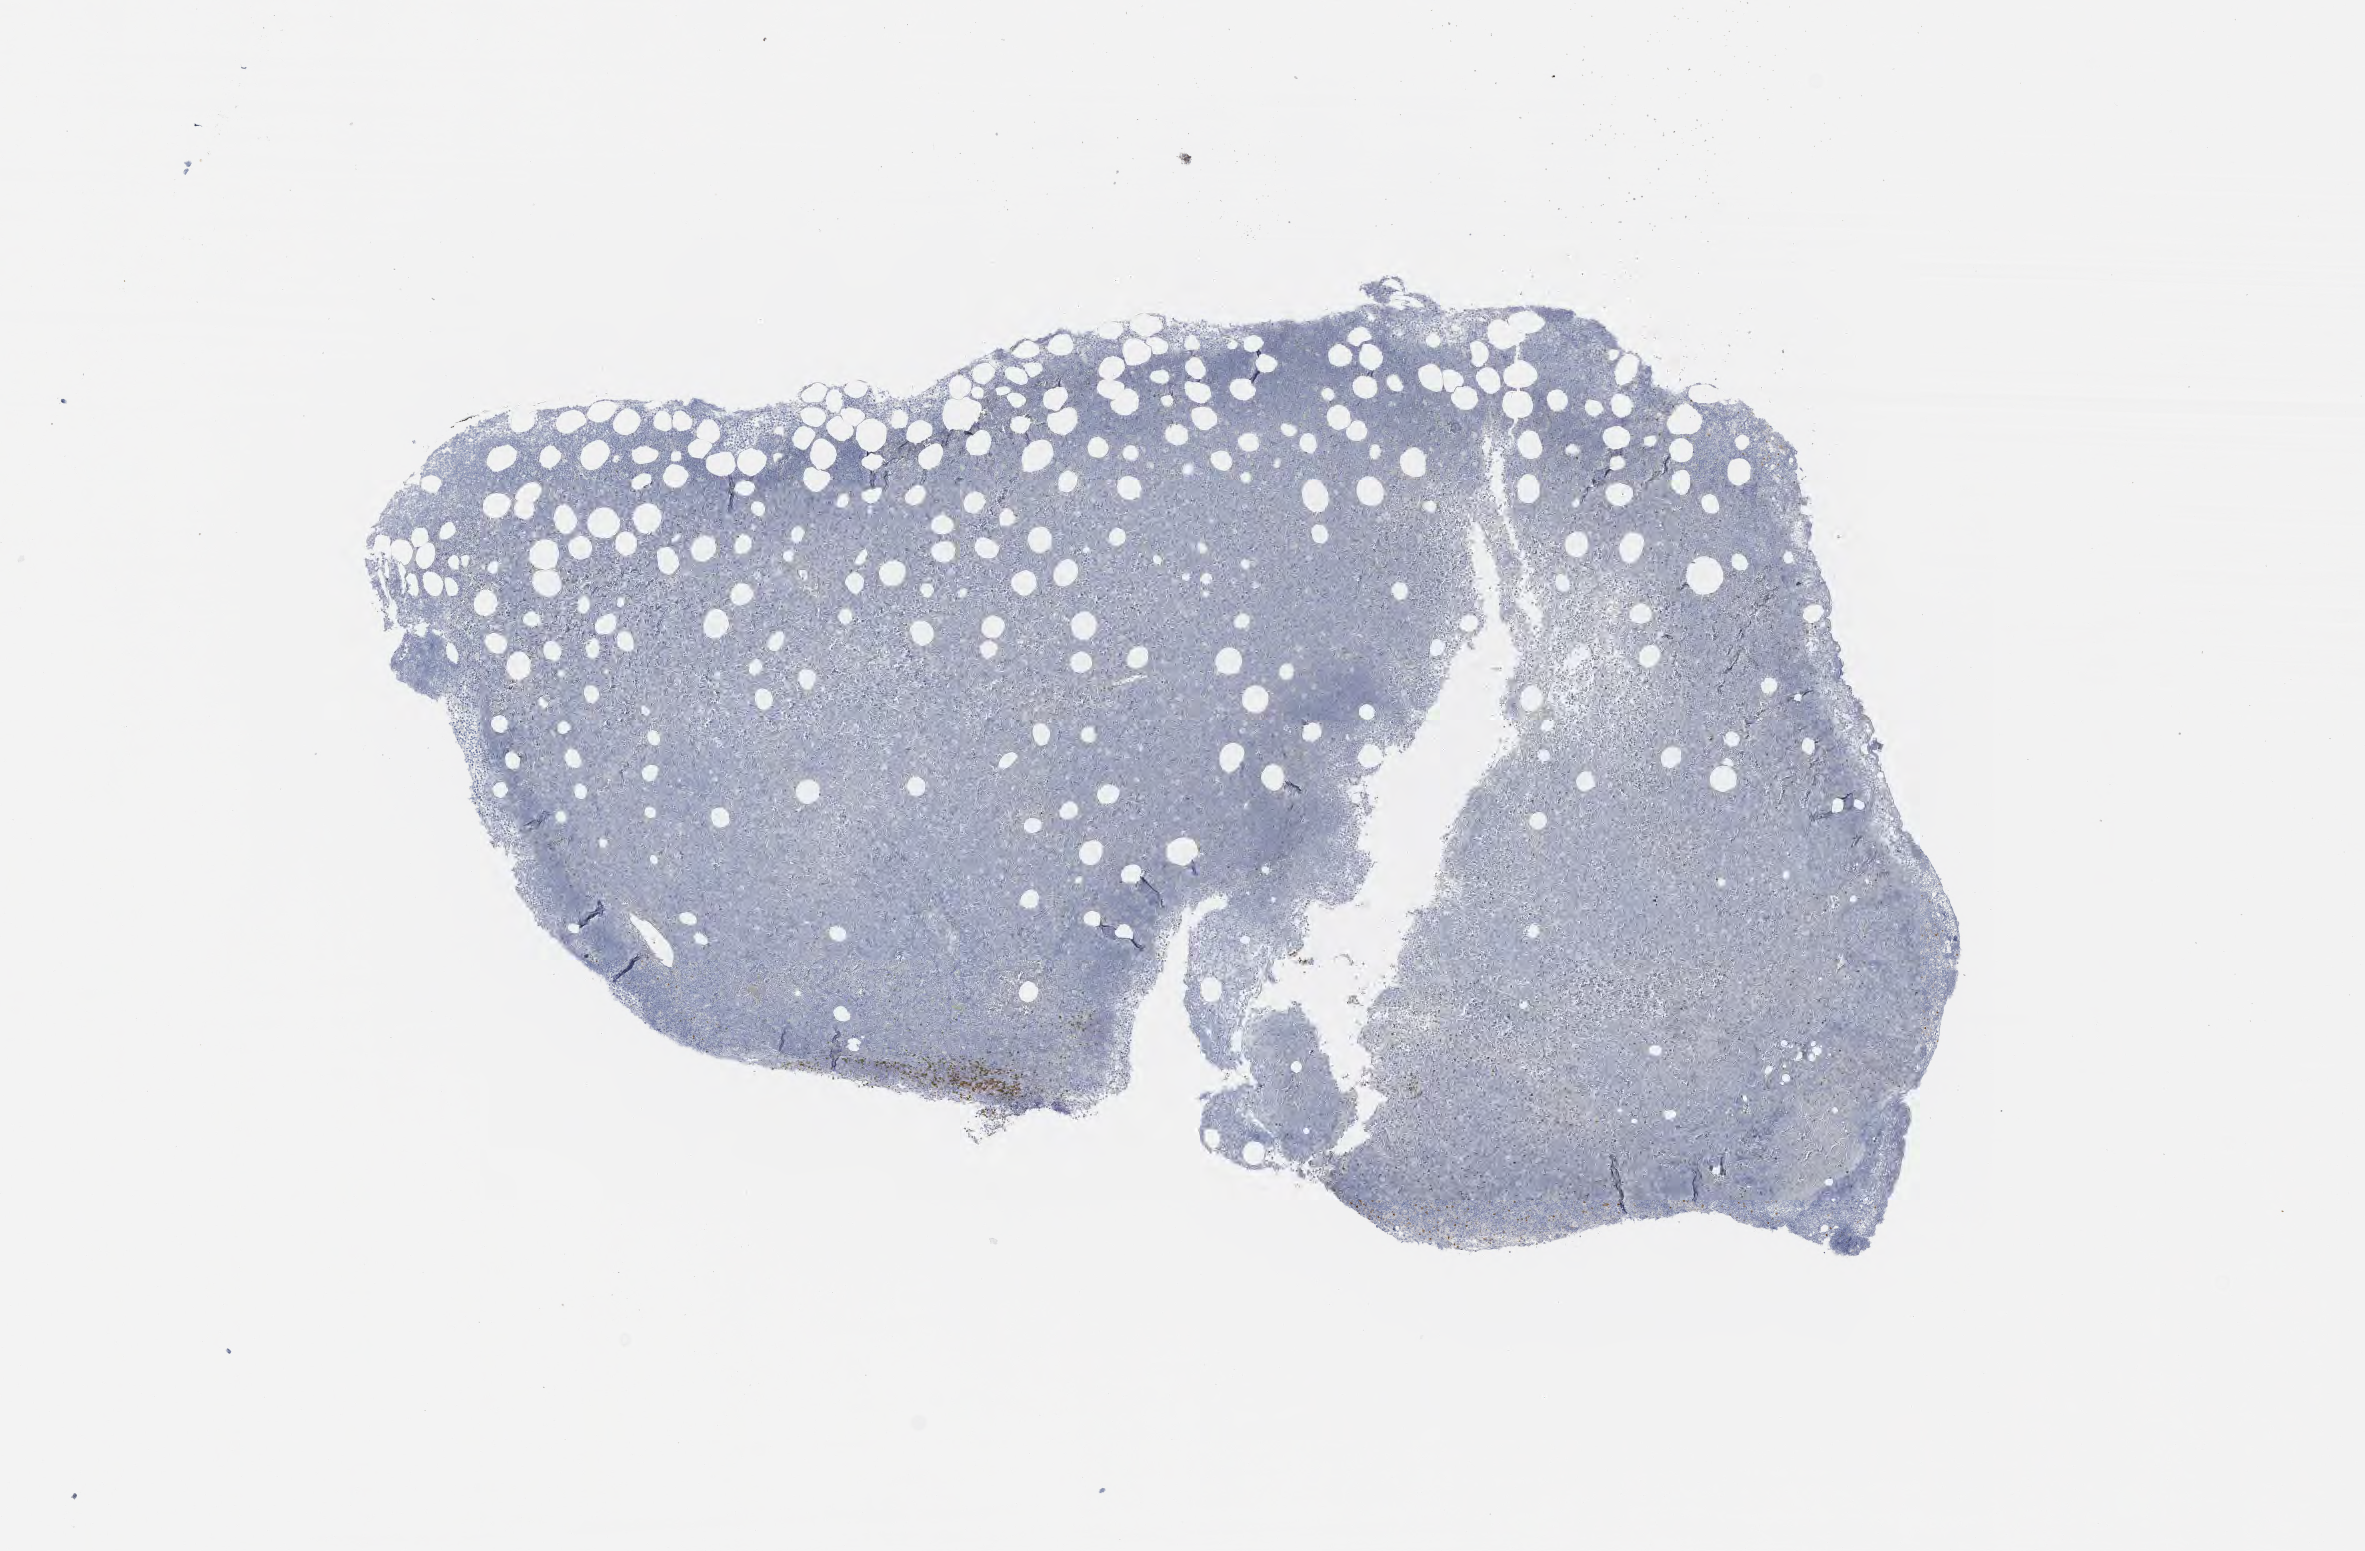
IHC for BCL2, whole-slide image, a low-resolution overview of the entire scanned area, about 9.6 x 6.3 mm. Tumor tissue. Anatomic site: bone marrow. Patient male; 70 years old.
• diagnosis: Neoplasm, uncertain whether benign or malignant